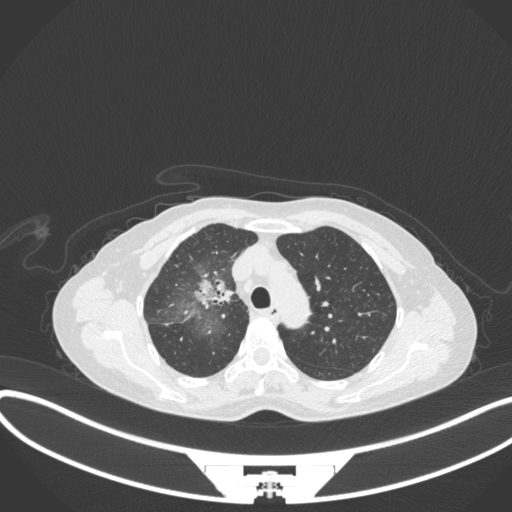
Chest CT, one axial slice. Position 233 of 311 along the scan axis. Reconstruction kernel B31f. 120 kVp. Lung window (W 1500 / L -600 HU). 1 mm slice thickness. 512 × 512 image matrix, field of view 400 × 400 mm. Female patient, age 59 years. From the clinical record (not read from this slice): clinical TNM (as recorded): T3 N0 M0; histopathological grade: G1.
Outlined on this slice (rectangle marked by the reading radiologist):
- lung tumour (recorded histology: adenocarcinoma): bounding box [x1, y1, x2, y2] px = [189, 272, 234, 317]